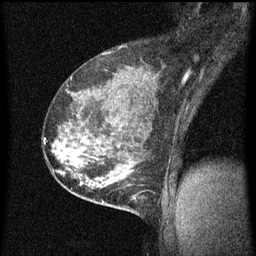
Breast MRI (dynamic contrast-enhanced), one sagittal slice. Slice 40 of 60 in the series (ordered by position). Dynamic contrast-enhanced series, image 2 of 3 at this slice position (ordered by acquisition). 1.5 T. TE 4.2 ms, TR 8 ms. 2 mm slice thickness. 256 × 256 image matrix. Patient: female, 35 years.
Structures marked on this image (semi-automatic segmentation, software-assisted and operator-edited):
- analysis volume of interest (the breast-tissue region the enhancement analysis was run in; not a lesion): bounding box [x1, y1, x2, y2] px = [110, 178, 156, 217]
- tumour enhancement mask (voxels above the 70 % enhancement threshold inside the analysis volume of interest): [110, 178, 143, 201]